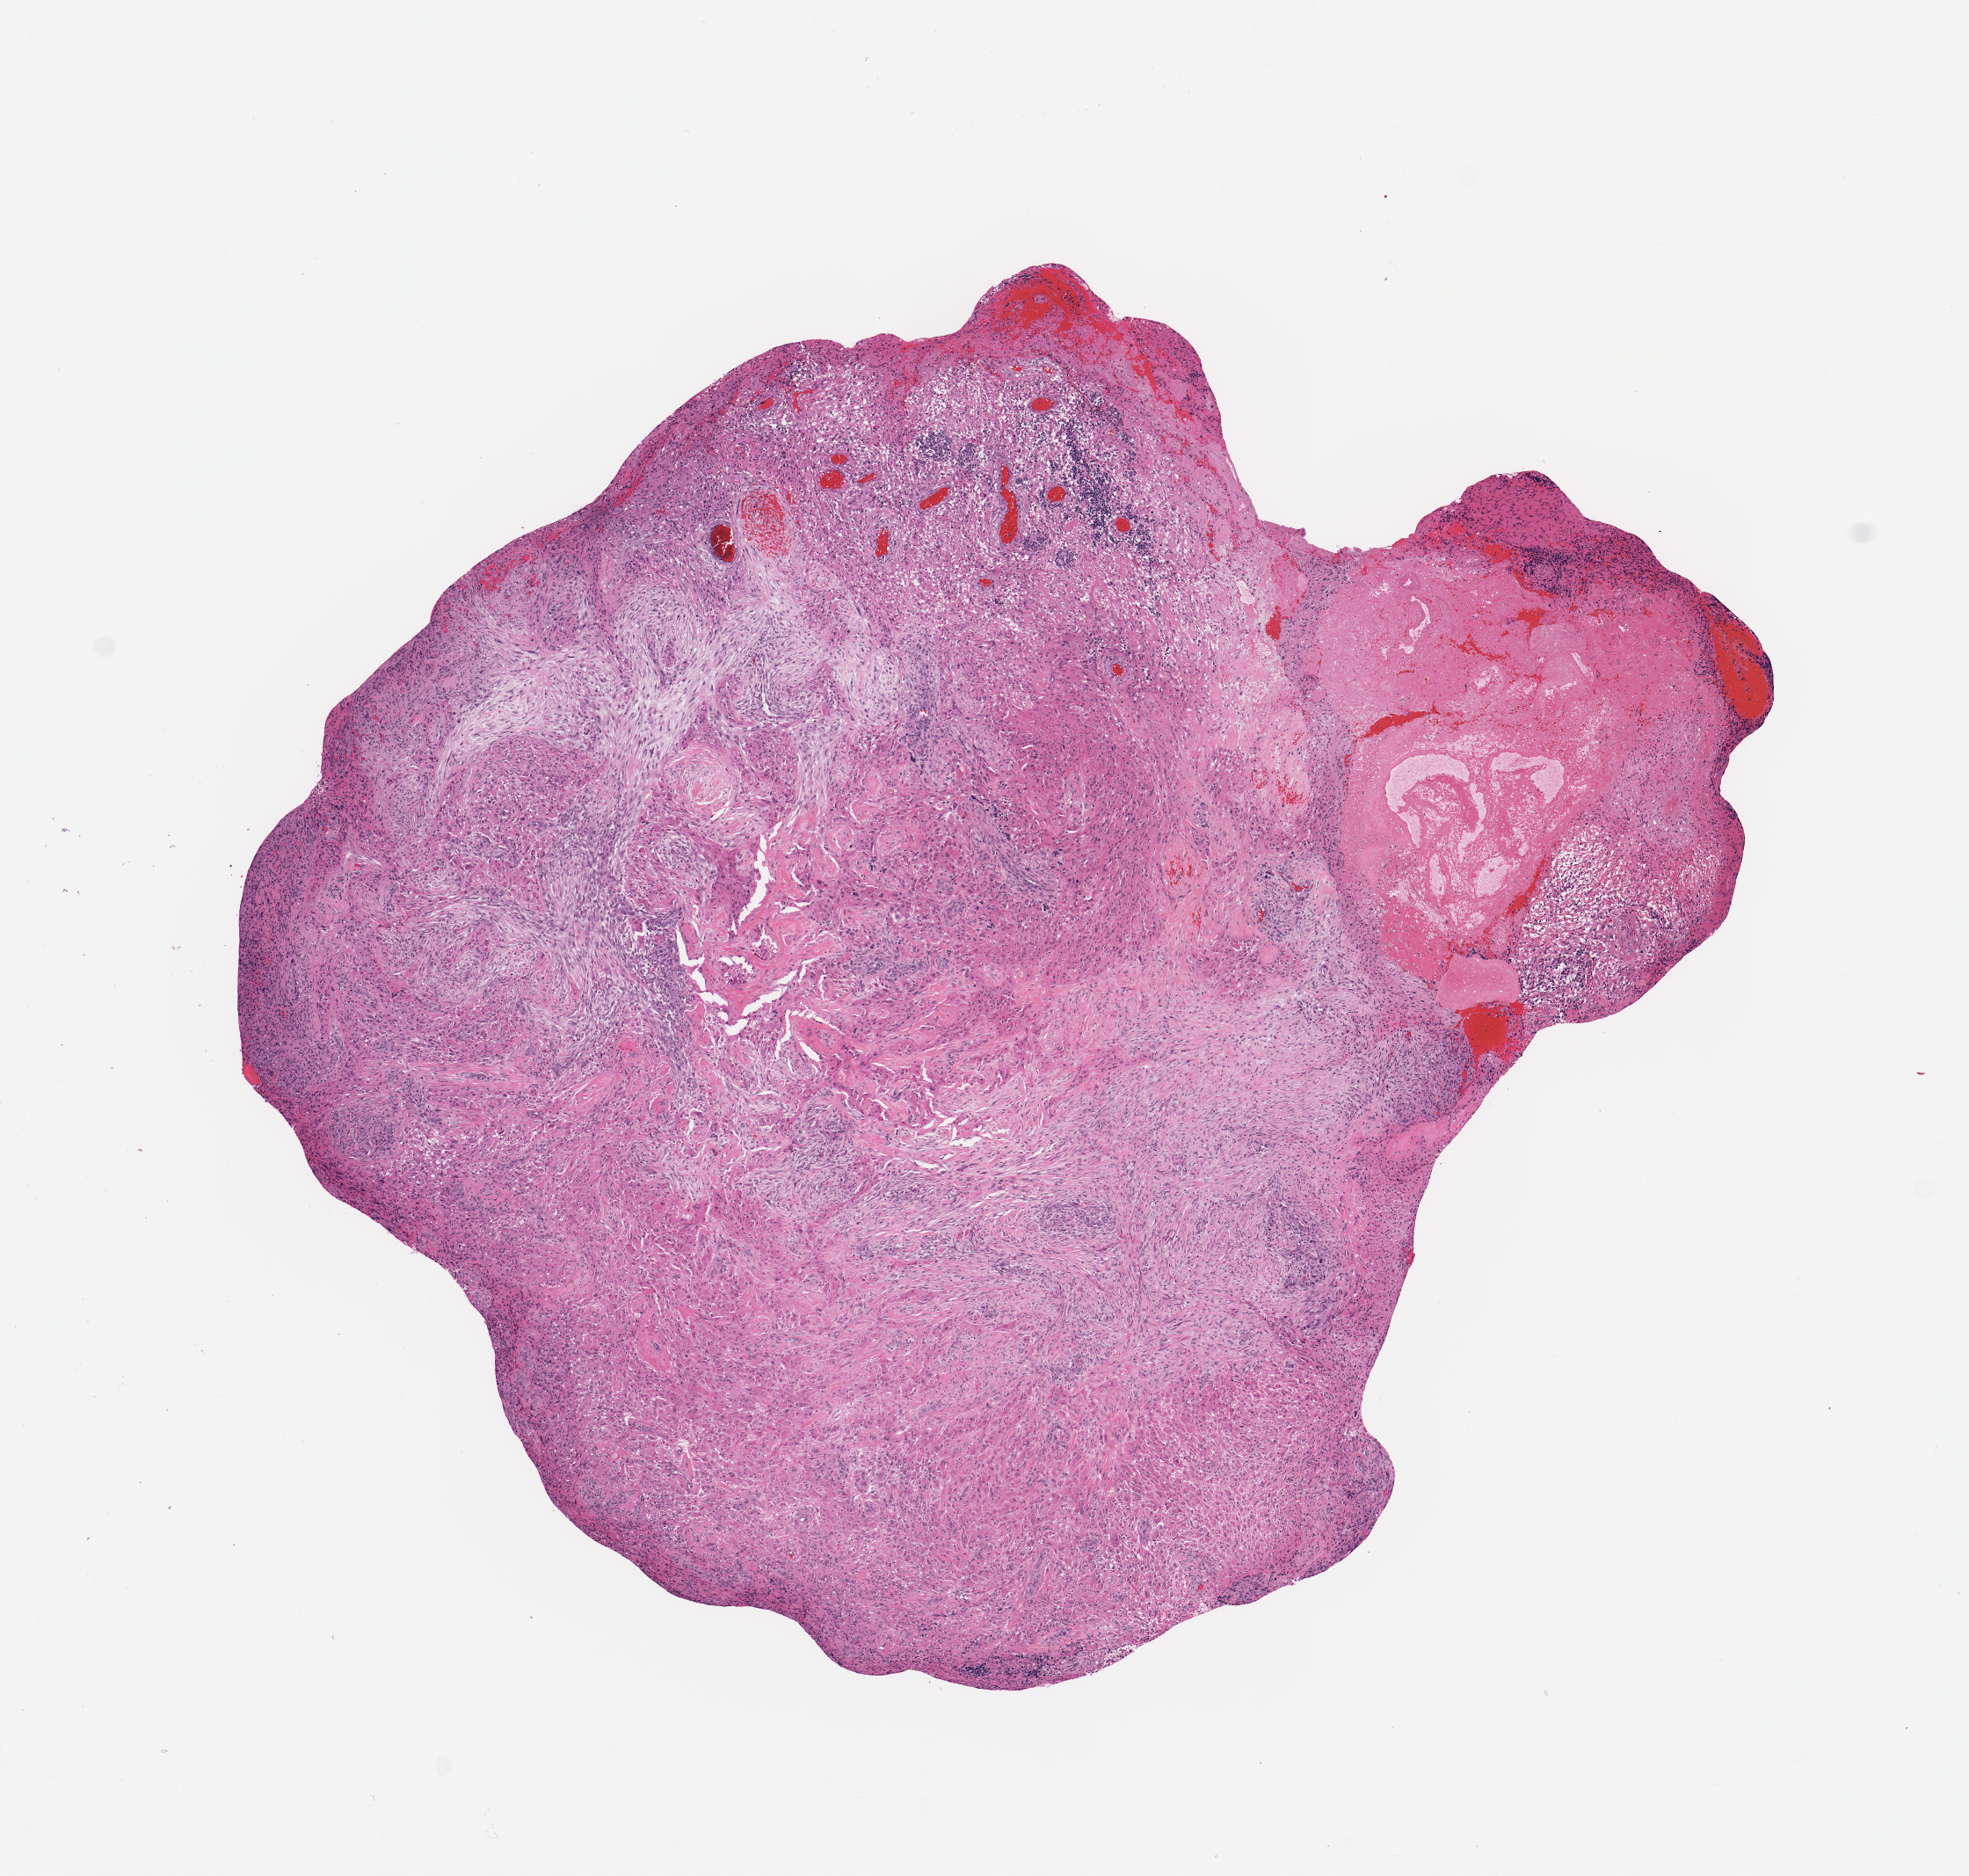
Digitized H&E-stained tissue section (whole slide), low-resolution overview of the scanned area, about 8.9 x 8.4 mm (from a 20x scan). Tumour tissue sample, sampled site: frontal lobe. Male, 46 y/o. Pathologist review of this section (percent, as recorded): tumour nuclei 60%, necrosis 15%.
Histologic diagnosis: Glioblastoma.